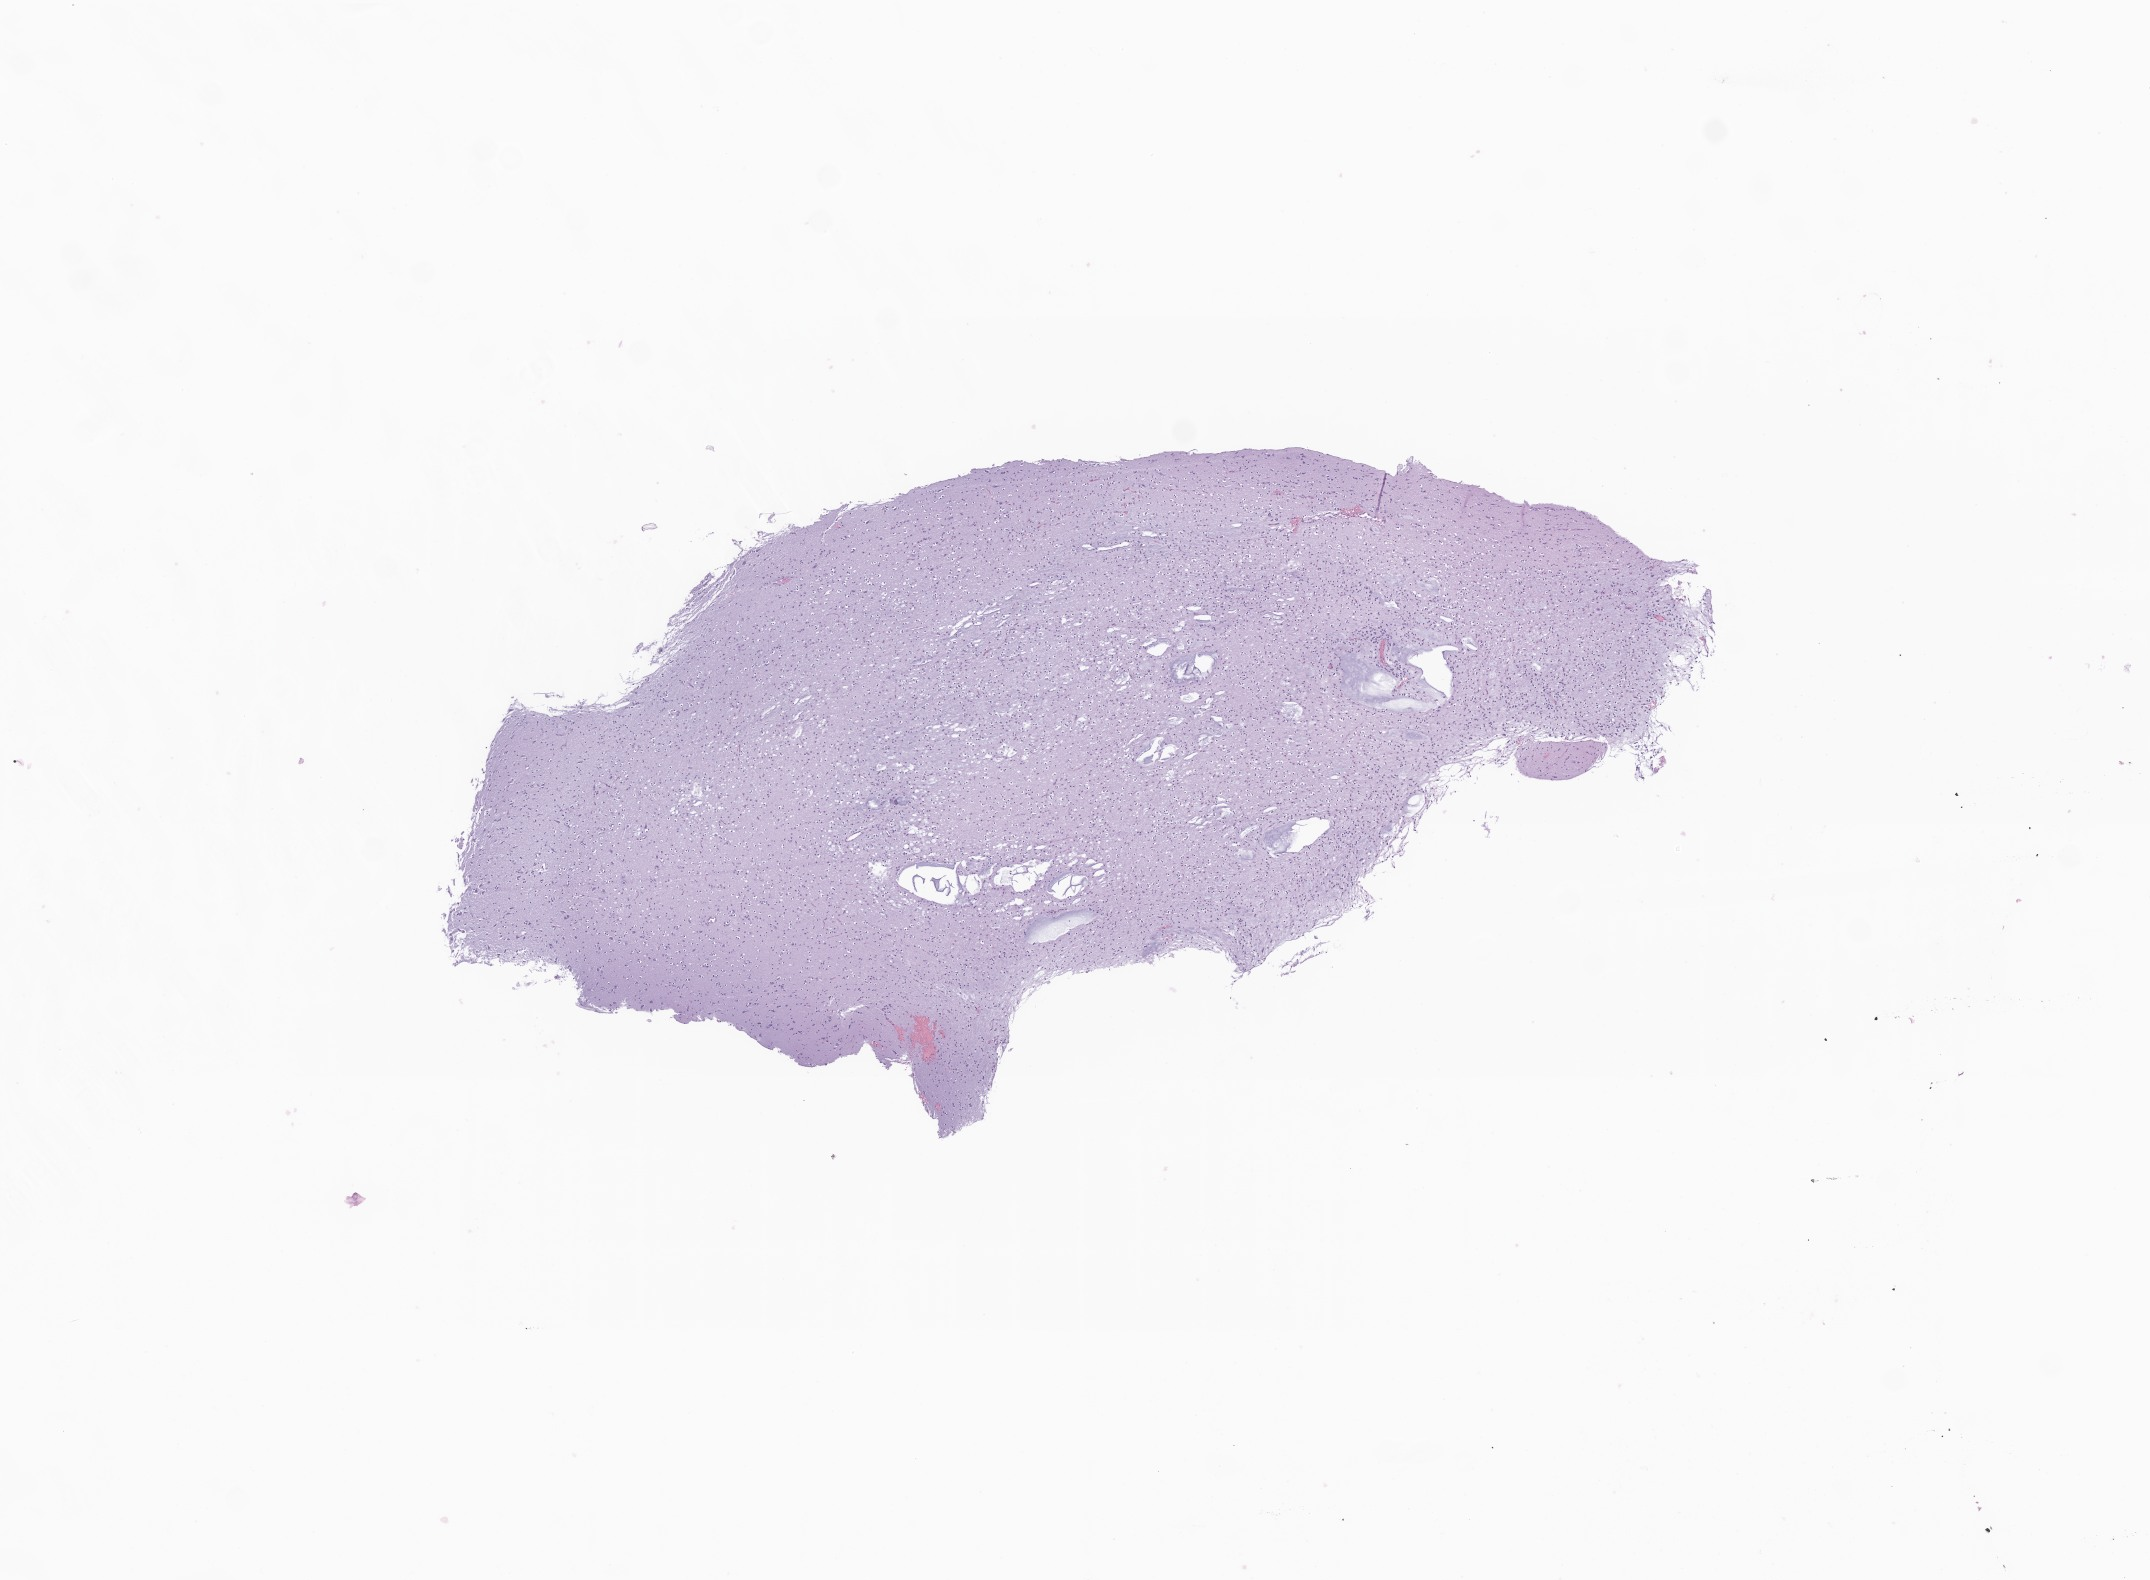
Whole-slide image, hematoxylin and eosin (H&E) stain of tumor tissue from the temporal lobe — shown as a low-resolution overview of the whole scanned area (about 9.1 x 6.7 mm), formalin-fixed, paraffin-embedded (FFPE) tissue. Patient: male, age 240 months (20 years).
Recorded diagnosis: Dysembryoplastic neuroepithelial tumor.